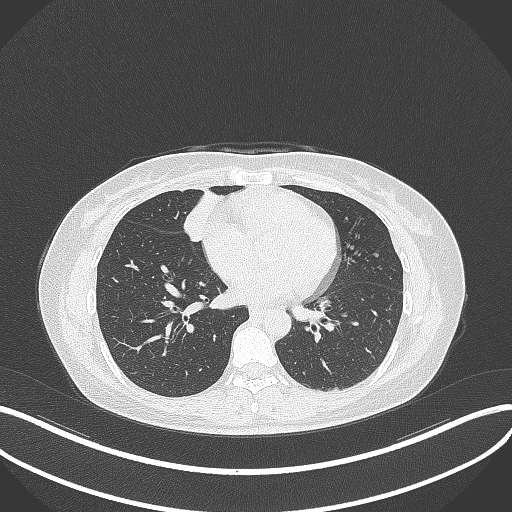
Chest CT, one axial slice; slice 114 of 284 in the series (ordered by position); 120 kVp; lung window (W 1500 / L -600 HU); 512 × 512 image matrix, field of view 400 × 400 mm. Patient: female, 43 years. Case-level facts recorded for this patient, not image findings: clinical TNM (as recorded): T1c N3 M1.
Structures marked on this image (bounding box drawn by a radiologist):
- lung tumour (recorded histology: adenocarcinoma): bounding box [x1, y1, x2, y2] px = [180, 194, 216, 250]